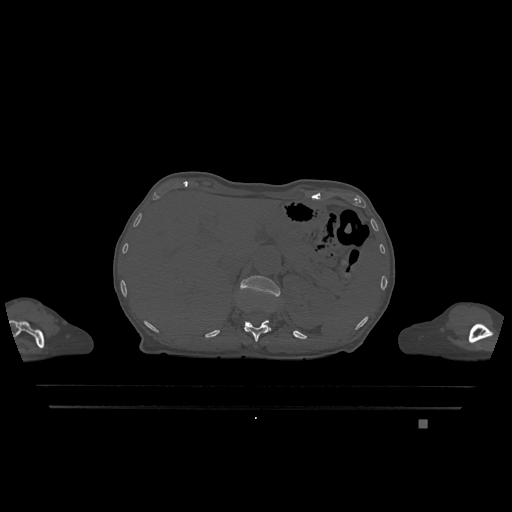
CT including the spine, one axial slice. Position 516 of 1317 along the scan axis. Bone window (W 1800 / L 400 HU). 0.5 mm slice thickness. 512 × 512 image matrix. Female patient, age 74 years. From the clinical record (not read from this slice): primary cancer: lung; vertebrae with lytic lesions (as recorded): T1, T4, T5, T6, L4, L5.
Structures marked on this image (semi-automatic segmentation, software-assisted and operator-edited):
- L1 vertebra: bounding box <240,276,280,330> (left, top, right, bottom; pixels)
- T12 vertebra: <244,320,270,342>